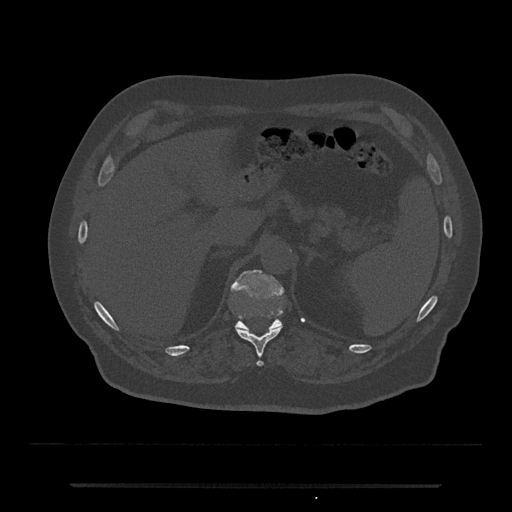
CT including the spine, one axial slice; slice 629 of 797 in the series (ordered by position); bone window (W 1800 / L 400 HU); 0.5 mm slice thickness; 512 × 512 image matrix, field of view 434 × 434 mm. Male patient, age 80 years. Case-level facts recorded for this patient, not image findings: primary cancer: prostate.
Annotated regions visible in this slice (semi-automatic segmentation, software-assisted and operator-edited):
- T11 vertebra: box from (x=236, y=327) to (x=282, y=367) px
- T12 vertebra: (x=231, y=269)–(x=284, y=331)